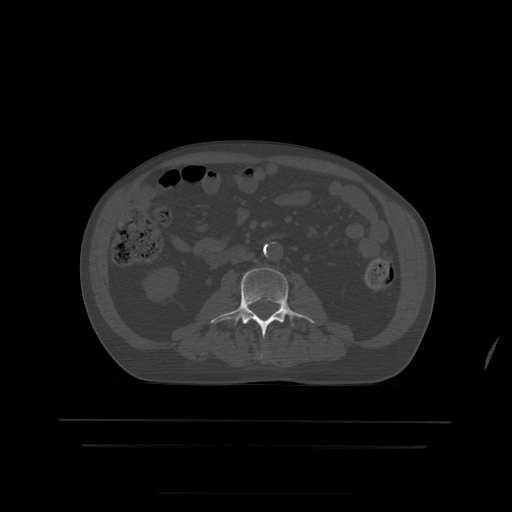
CT including the spine, one axial slice; slice 121 of 522 in the series (ordered by position); bone window (W 1800 / L 400 HU); 512 × 512 image matrix. Patient age 68 years. From the clinical record (not read from this slice): primary cancer: urothelial.
Outlined on this slice (semi-automatic segmentation, software-assisted and operator-edited):
- L2 vertebra: bounding box [x1, y1, x2, y2] px = [259, 352, 264, 359]
- L3 vertebra: [211, 268, 315, 337]